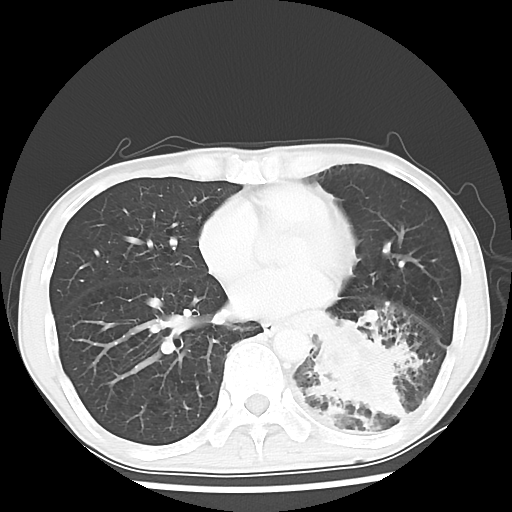
Chest CT, one axial slice; slice 25 of 64 in the series (ordered by position); lung window (W 1500 / L -600 HU); 512 × 512 image matrix, field of view 313 × 313 mm. Male patient, age 68 years. From the clinical record (not read from this slice): clinical TNM (as recorded): T4 N0 M0.
Structures marked on this image (bounding box drawn by a radiologist):
- lung tumour (recorded histology: squamous cell carcinoma): bounding box <292,294,413,439> (left, top, right, bottom; pixels)